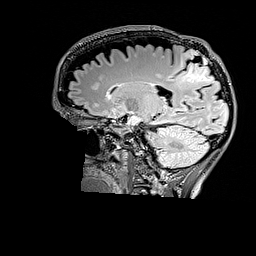
Brain MRI from a brain-tumour surgery series, one sagittal slice. Position 106 of 176 along the scan axis. T2 FLAIR. 256 × 256 image matrix. From the clinical record (not read from this slice): histopathology: Astrocytoma; WHO grade: 3; IDH mutation: yes.
Outlined on this slice (manually delineated by an expert):
- tumour: bounding box [x1, y1, x2, y2] px = [177, 49, 213, 86]
- tumour: [185, 58, 213, 83]